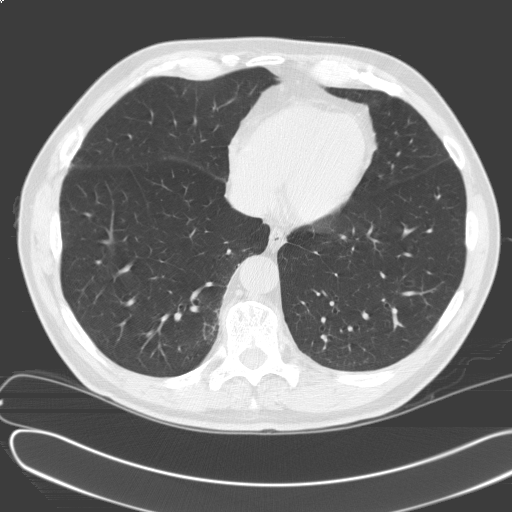
Chest CT (low-dose screening protocol), one axial image. Baseline annual screen. Lung window (W 1500 / L -600 HU). Standard (soft-tissue) reconstruction kernel (C). Slice 51 of 164 in the series. Male, age 69 years at enrolment.
- Expert reader's lesion annotation, bounding box [x1, y1, x2, y2] px = [234, 113, 262, 141].
- The screening reader recorded 2 non-calcified nodules or masses ≥4 mm on this exam (left upper lobe, right lower lobe); which of them this box marks is not recorded.
- Official screen result: positive, change unspecified: nodule(s) >= 4 mm or enlarging nodule(s), mass(es), or other non-specific abnormalities suspicious for lung cancer.
- Participant outcome: lung cancer diagnosed 450 days after this screen (after the second annual screen) — adenosquamous carcinoma, right upper lobe, poorly differentiated (G3), stage IV (AJCC 6th edition), 30 mm at pathology.